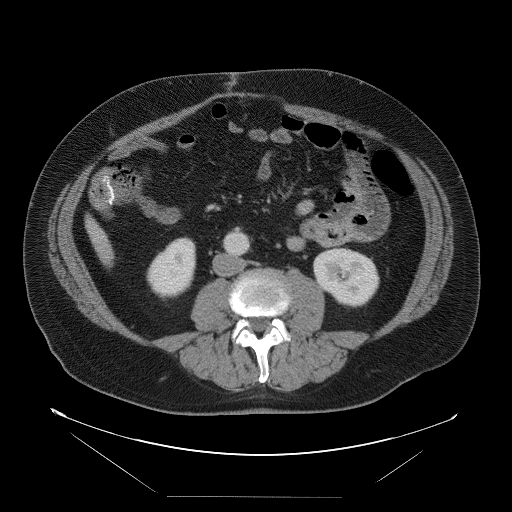
Contrast-enhanced abdominal CT, one axial slice. Position 13 of 114 along the scan axis. 120 kVp. Intravenous contrast given. Soft-tissue window (W 400 / L 40 HU). 5 mm slice thickness. 512 × 512 image matrix. Male patient, age 61 years. Case-level facts recorded for this patient, not image findings: diagnosis: colorectal cancer liver metastases, imaged before liver resection.
Outlined on this slice (manually delineated by an expert):
- liver: bounding box <89,223,113,264> (left, top, right, bottom; pixels)